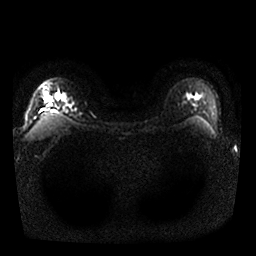
Breast MRI, one axial slice. Slice 21 of 25 in the series (ordered by position). Diffusion-weighted series; image 2 of 4 stored at this slice position (different b-values; order by instance number). 1.5 T. 256 × 256 image matrix, field of view 340 × 340 mm. Female patient.
Outlined on this slice (outlined manually by an expert reader):
- tumour on diffusion-weighted imaging: bounding box (x1, y1, x2, y2) in pixels: (45, 93, 49, 98)